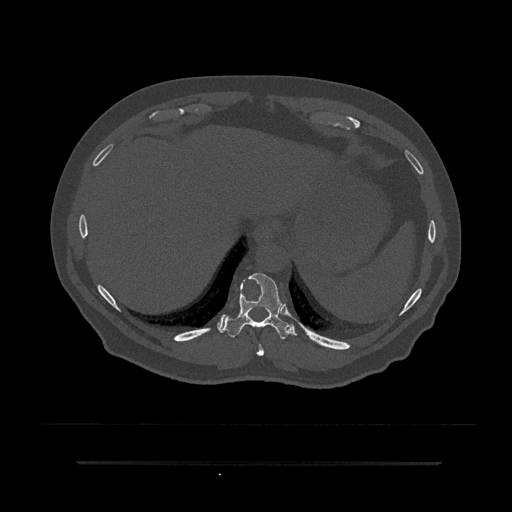
CT including the spine, one axial slice. Position 332 of 797 along the scan axis. Bone window (W 1800 / L 400 HU). 512 × 512 image matrix, field of view 464 × 464 mm. Patient: male, 59 years. Case-level facts recorded for this patient, not image findings: primary cancer: bile ducts; vertebrae with lytic lesions (as recorded): T10.
Structures marked on this image (semi-automatically segmented with operator editing):
- T10 vertebra: bounding box (x1, y1, x2, y2) in pixels: (222, 273, 297, 339)
- T9 vertebra: (256, 344, 264, 356)